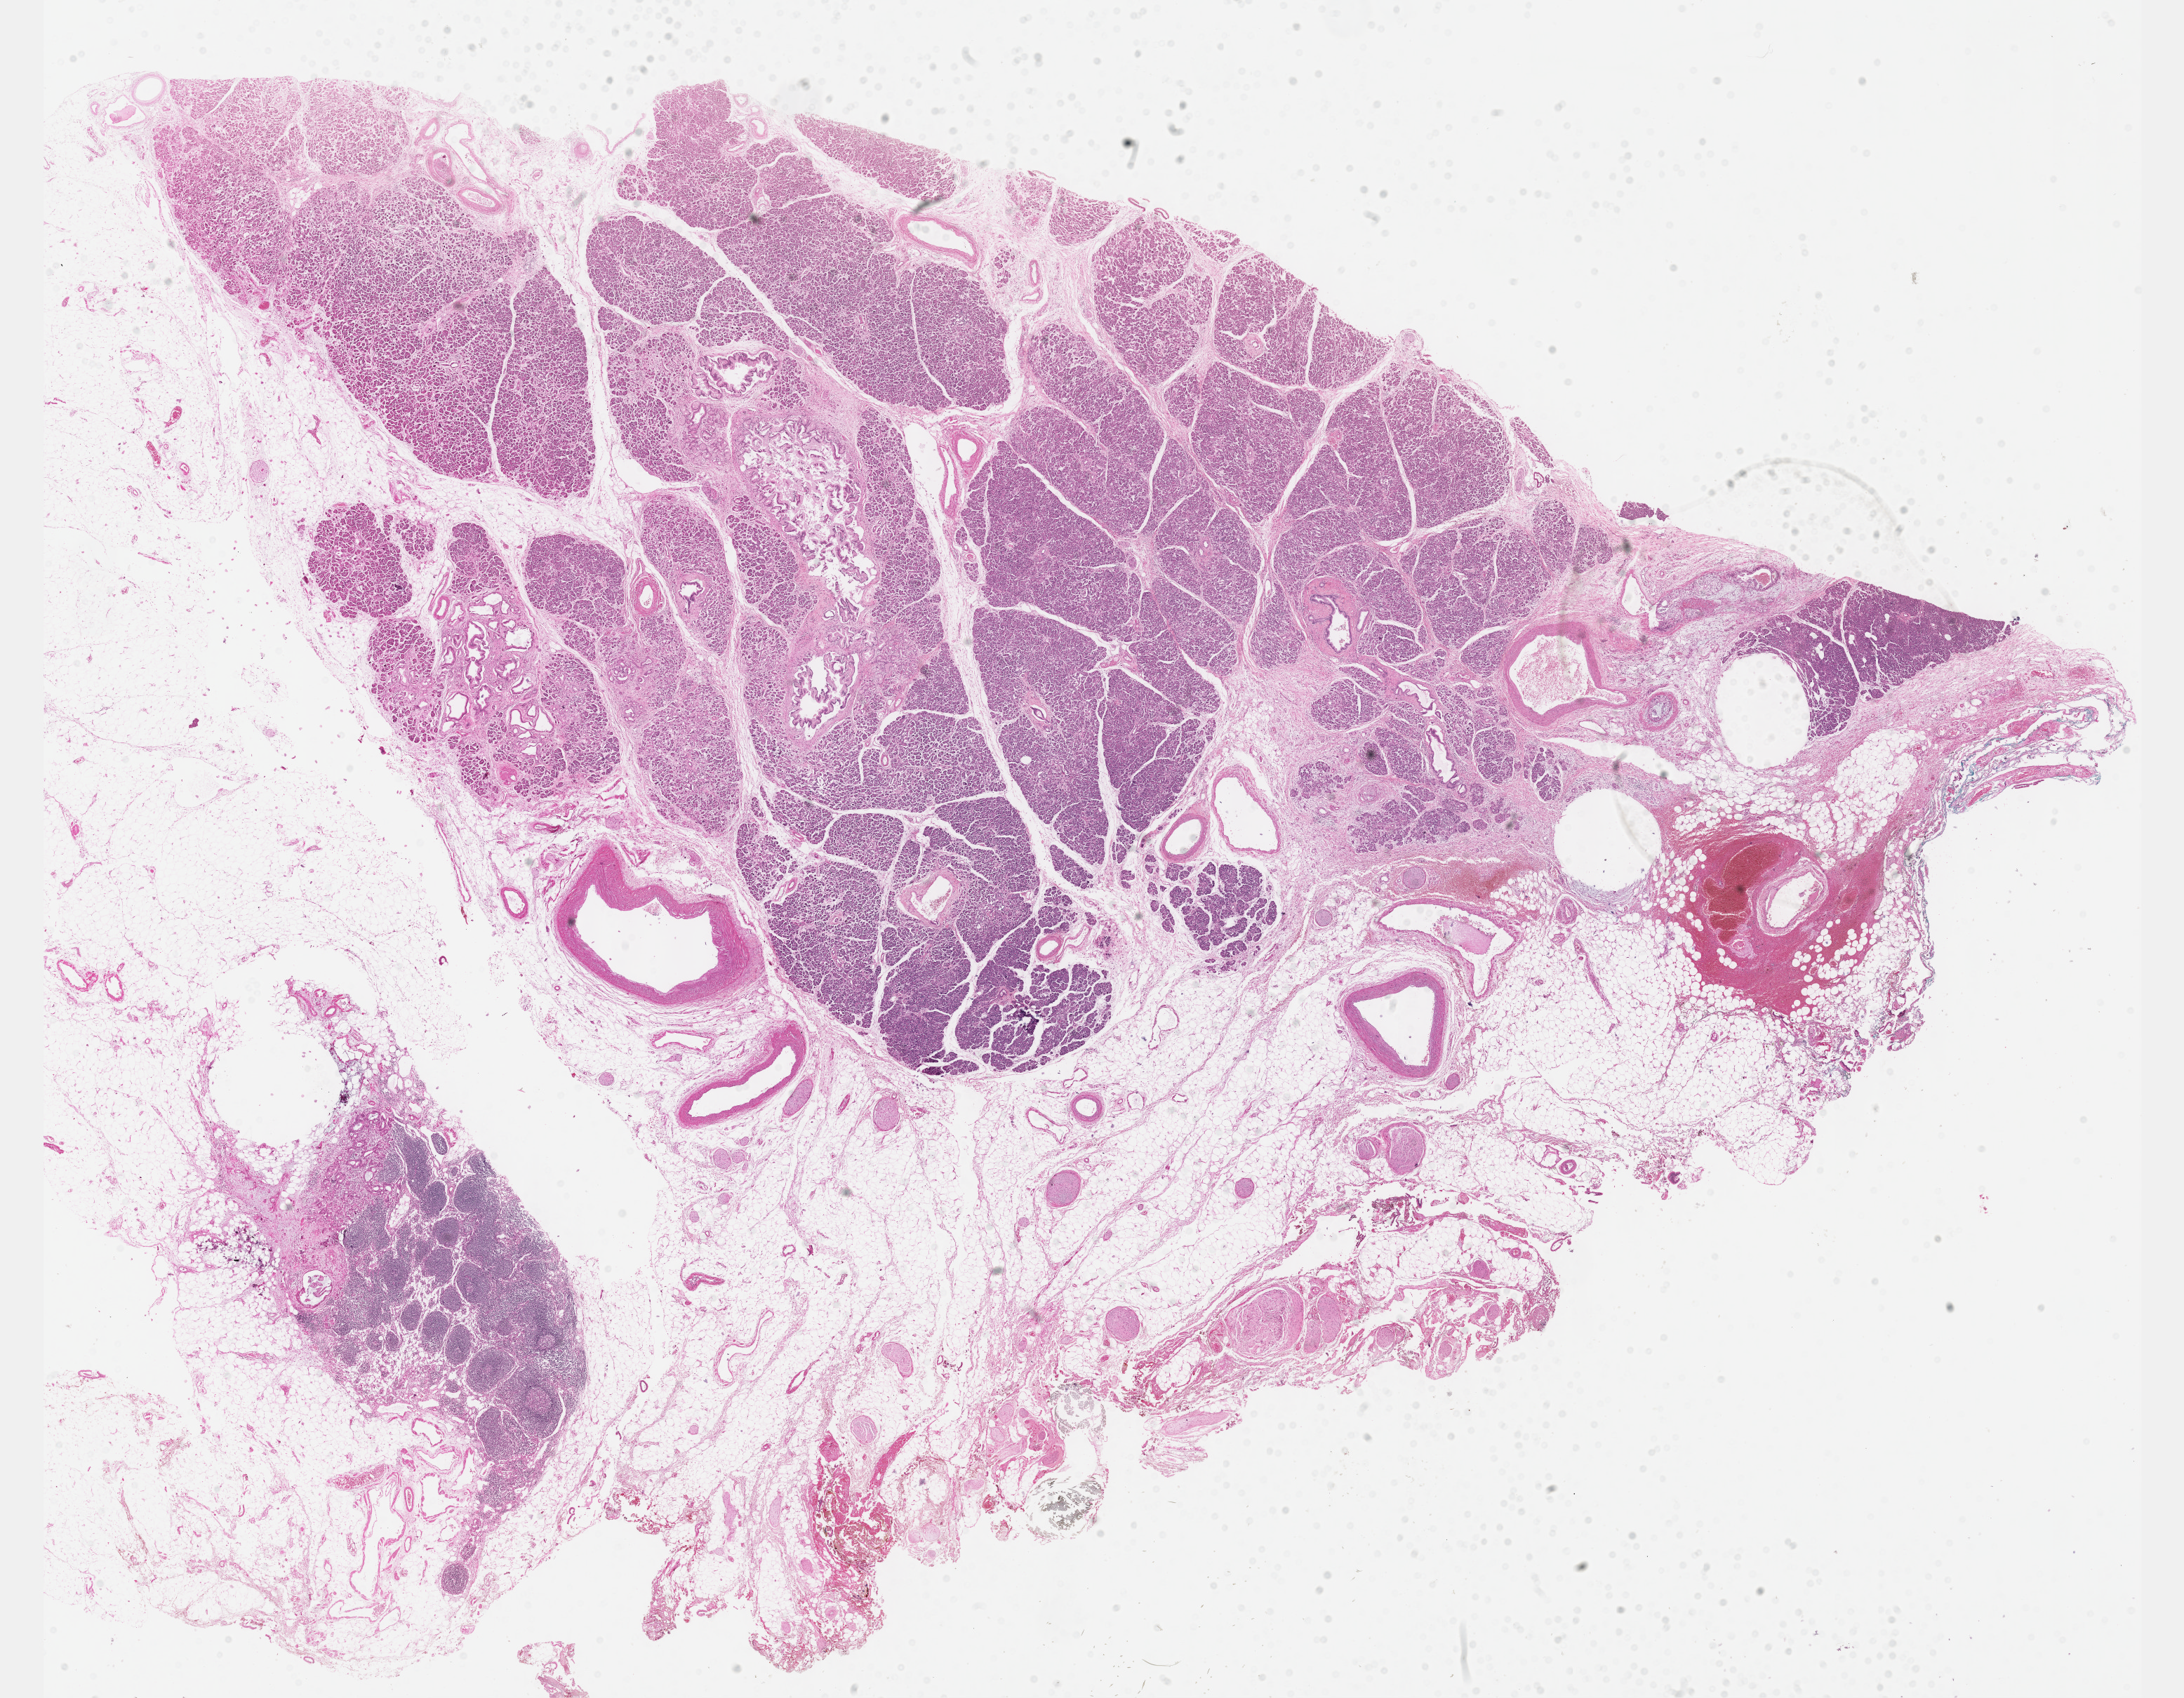
Hematoxylin and eosin (H&E) stained whole-slide image — whole scanned area (about 25.1 x 19.6 mm) shown as a low-resolution overview; FFPE section; sample: primary tumour, pancreas. Patient: female, age at initial diagnosis 76 years. Histologic grade: G3 (poorly differentiated).
Lymph nodes positive (case pathology): 2 of 17 examined. Histologic diagnosis: Infiltrating duct carcinoma, NOS (head of pancreas). TNM: T3 N1 MX. AJCC pathologic stage: IIB (7th edition).